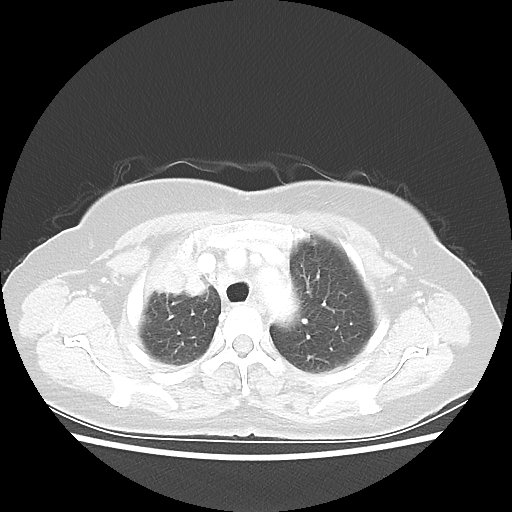
Chest CT, one axial slice; position 43 of 55 along the scan axis; 80 kVp; lung window (W 1500 / L -600 HU); 5 mm slice thickness; 512 × 512 image matrix. Female patient, age 62 years. From the clinical record (not read from this slice): clinical TNM (as recorded): T4 N3 M0.
Structures marked on this image (bounding box drawn by a radiologist):
- lung tumour (recorded histology: squamous cell carcinoma): bounding box <145,232,212,304> (left, top, right, bottom; pixels)